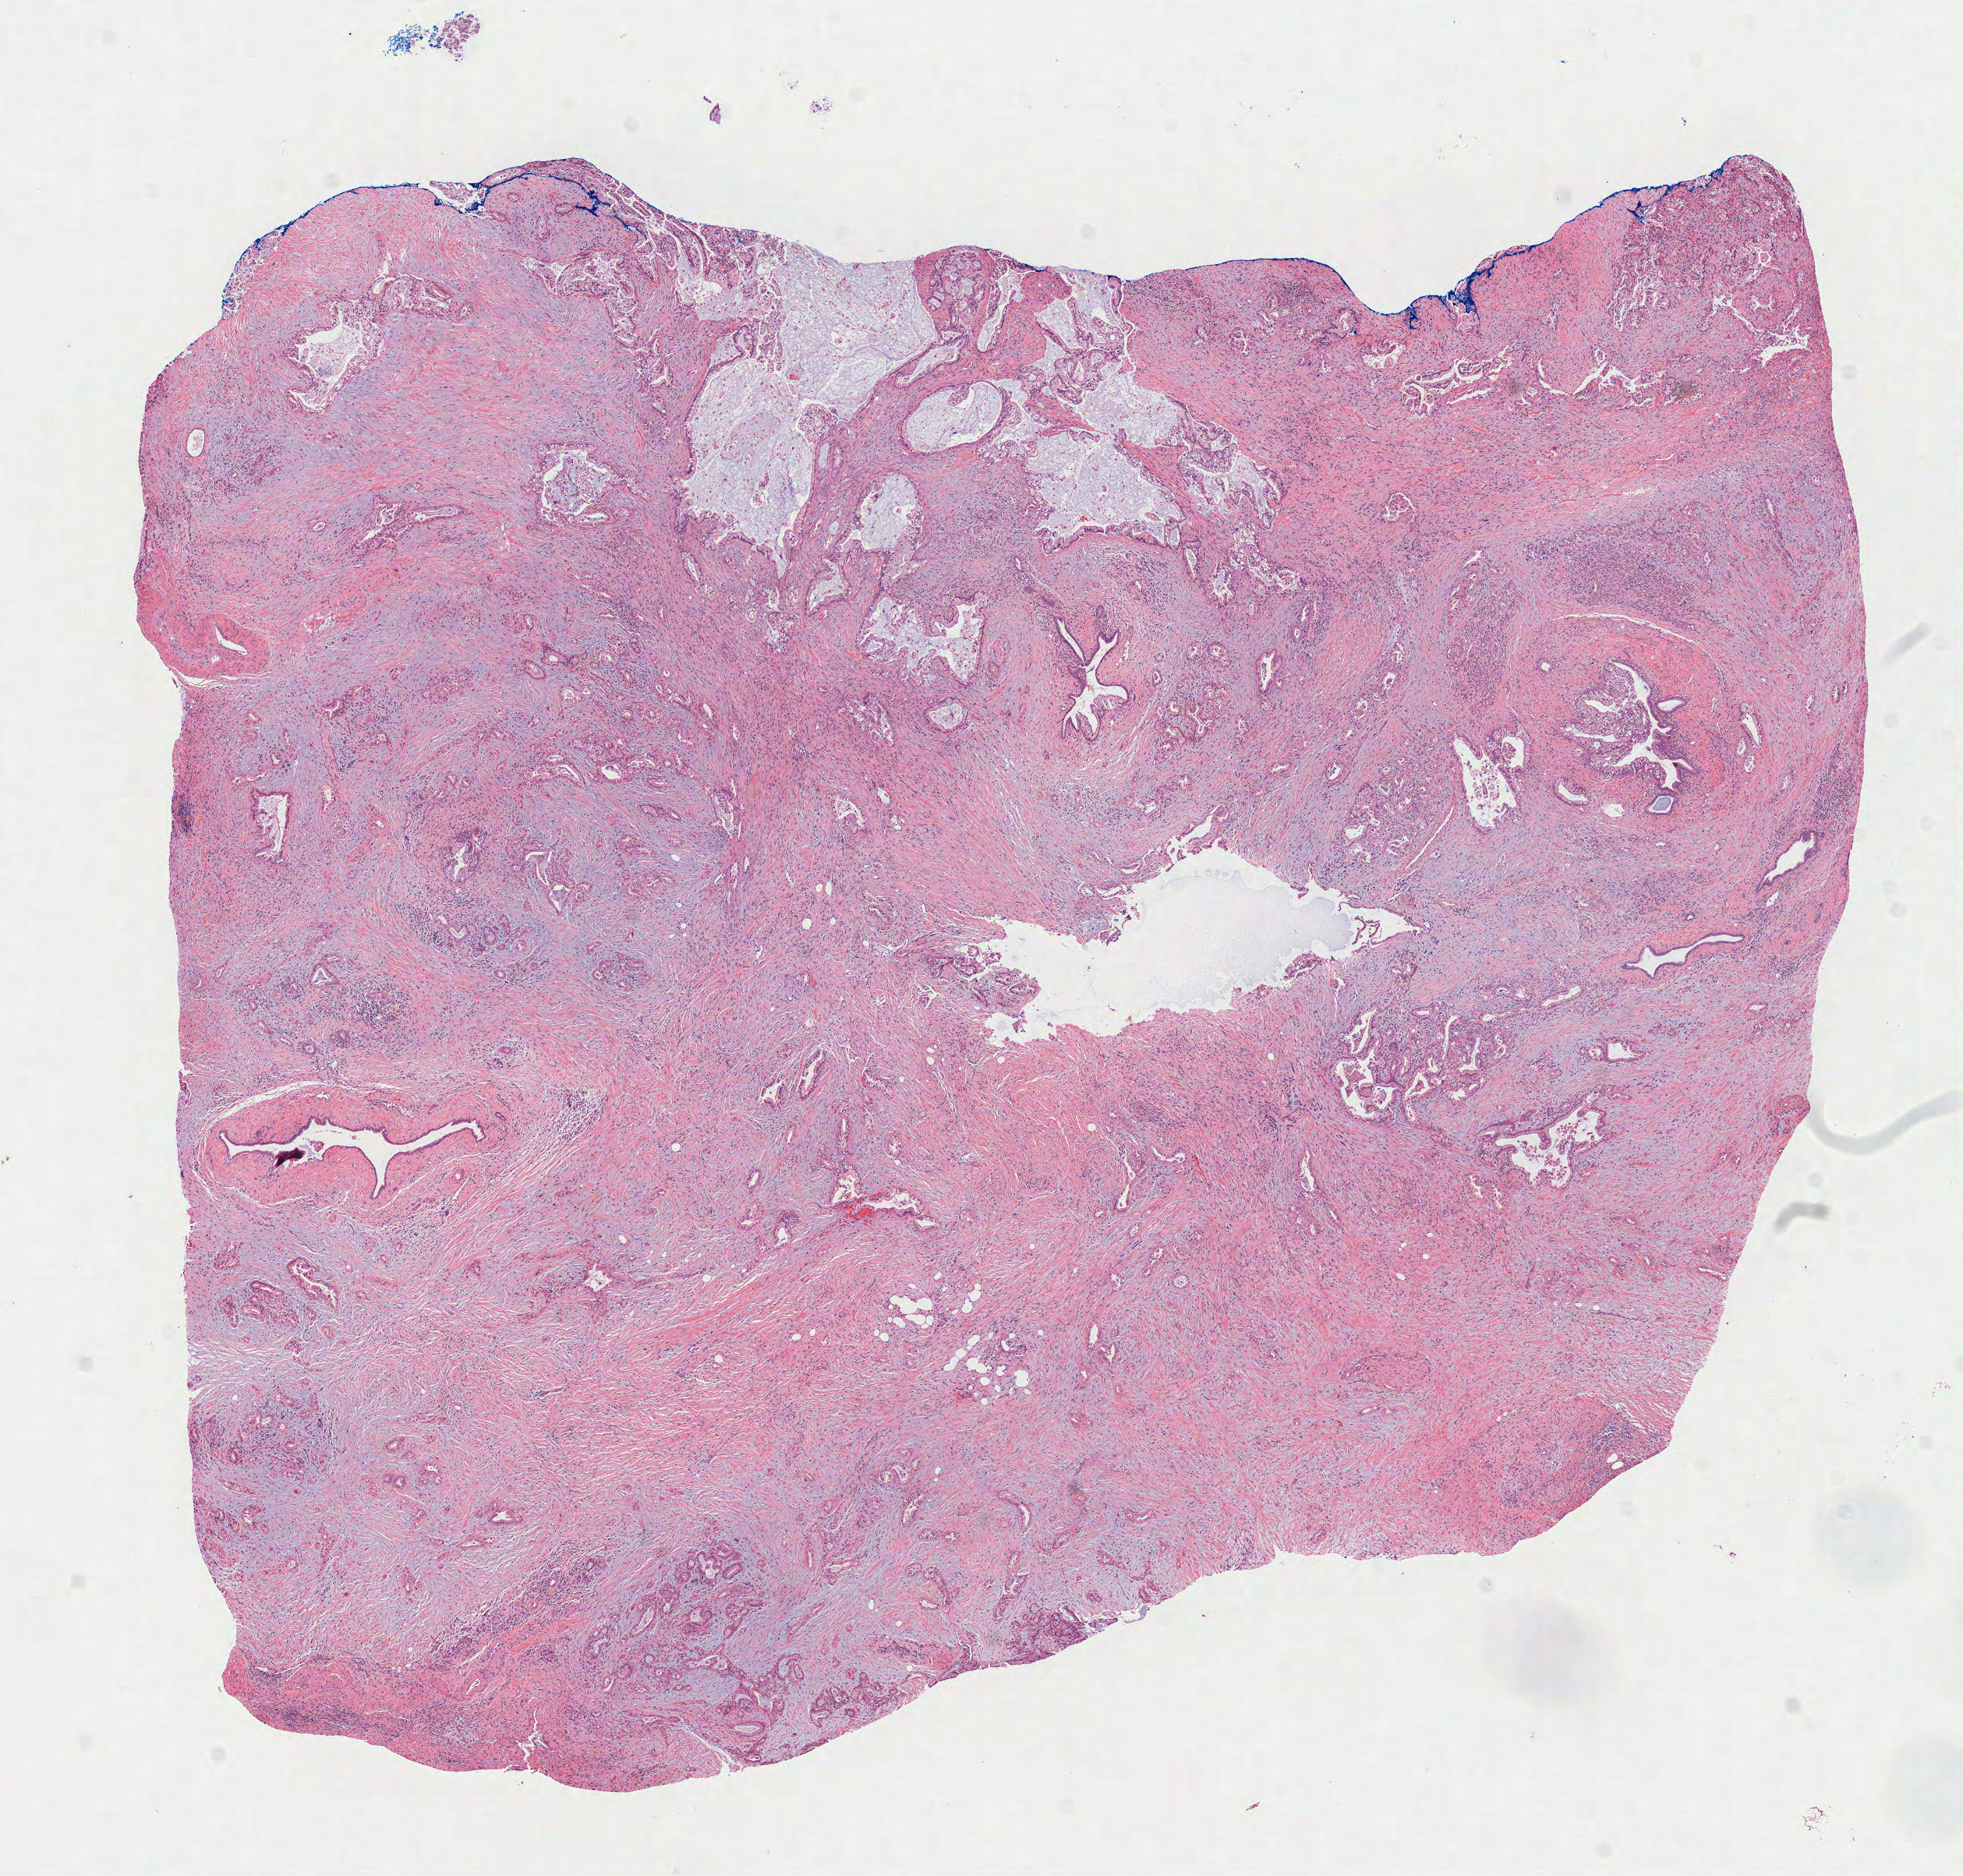
Whole-slide histology image, Hematoxylin and eosin (H&E) stained, shown as a low-resolution overview of the whole scanned area (about 10.2 x 9.7 mm, acquisition: 40x scan). Formalin-fixed paraffin-embedded (FFPE) diagnostic section. Sample: primary tumour, pancreas. Female patient; age at initial diagnosis 54 years. Histologic grade: G2 (moderately differentiated).
- diagnosis: Infiltrating duct carcinoma, NOS (head of pancreas)
- AJCC pathologic stage: IIA (7th edition)
- lymph nodes positive (case pathology): 0 of 21 examined